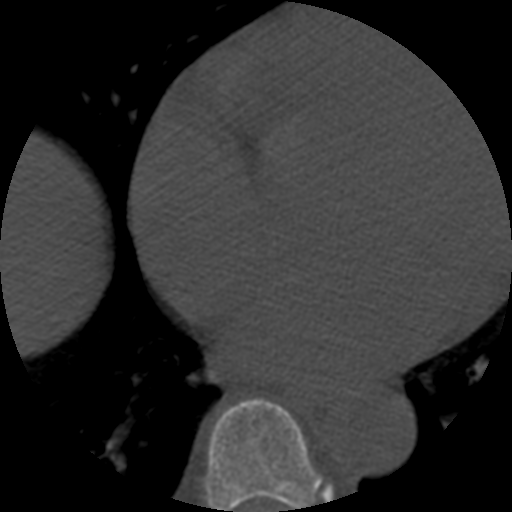
CT including the spine, one axial slice. Position 328 of 508 along the scan axis. Reconstruction kernel STANDARD. Bone window (W 1800 / L 400 HU). 1.25 mm slice thickness. 512 × 512 image matrix. Patient age 57 years. Case-level facts recorded for this patient, not image findings: primary cancer: prostate.
Structures marked on this image (semi-automatically segmented with operator editing):
- T7 vertebra: box from (x=204, y=399) to (x=323, y=512) px